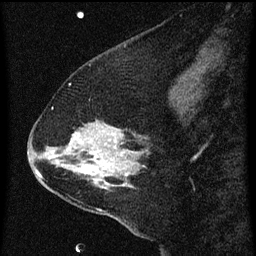
Breast MRI (dynamic contrast-enhanced), one sagittal slice. Slice 19 of 60 in the series (ordered by position). Dynamic contrast-enhanced series, image 2 of 3 at this slice position (ordered by acquisition). 1.5 T. TE 4.2 ms, TR 8 ms. 256 × 256 image matrix, field of view 180 × 180 mm. Female patient, age 47 years.
Annotated regions visible in this slice (semi-automatic segmentation, software-assisted and operator-edited):
- analysis volume of interest (the breast-tissue region the enhancement analysis was run in; not a lesion): box from (x=36, y=96) to (x=156, y=213) px
- tumour enhancement mask (voxels above the 70 % enhancement threshold inside the analysis volume of interest): (x=36, y=132)–(x=133, y=189)